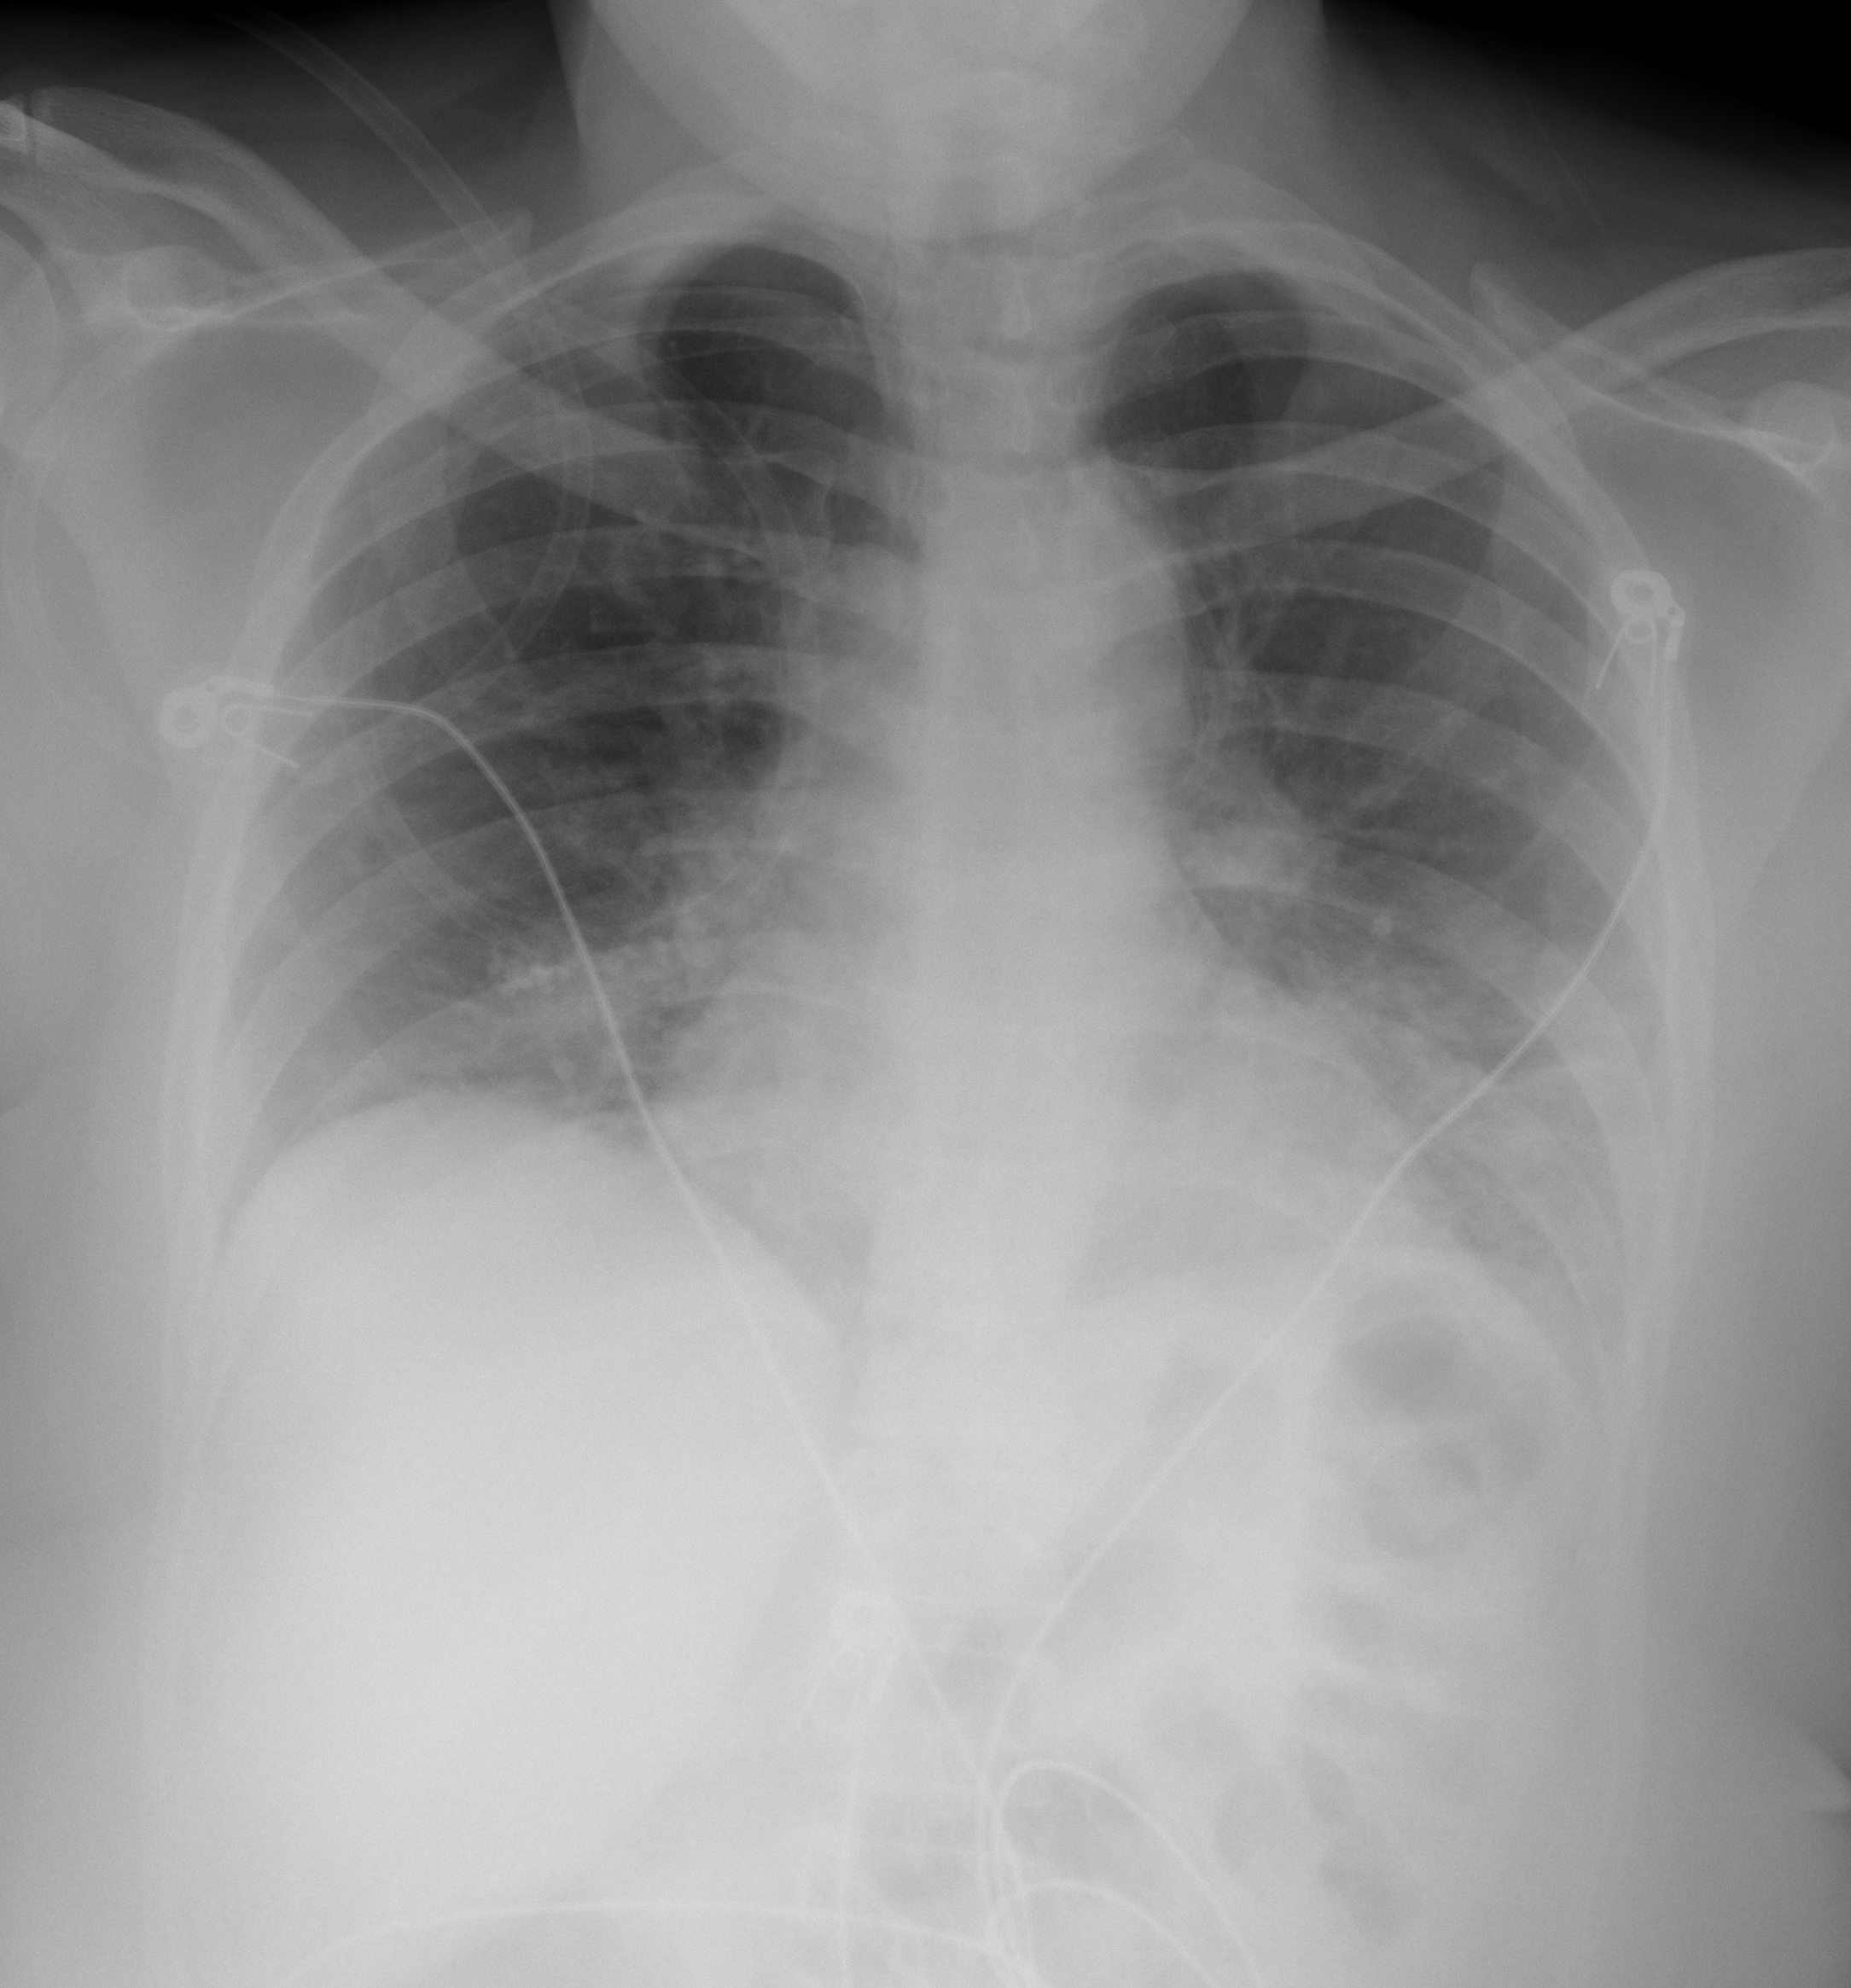
Chest X-ray (portable), AP projection. Female patient, age 58 years; imaged 0 days after the COVID-19 diagnosis.
Radiologist's key findings for this exam: diffuse opacities in the bilateral lung bases.